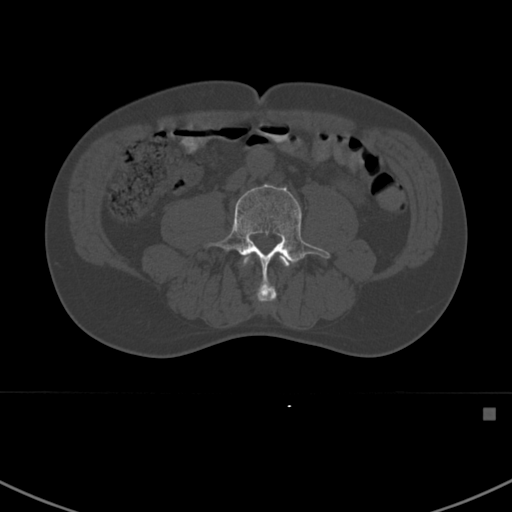
CT including the spine, one axial slice; position 245 of 412 along the scan axis; 120 kVp; bone window (W 1800 / L 400 HU); 1.5 mm slice thickness; 512 × 512 image matrix, field of view 358 × 358 mm. Patient: male, 59 years. From the clinical record (not read from this slice): primary cancer: prostate.
Annotated regions visible in this slice (semi-automatically segmented with operator editing):
- L3 vertebra: bounding box (x1, y1, x2, y2) in pixels: (242, 255, 293, 303)
- L4 vertebra: (207, 184, 330, 290)